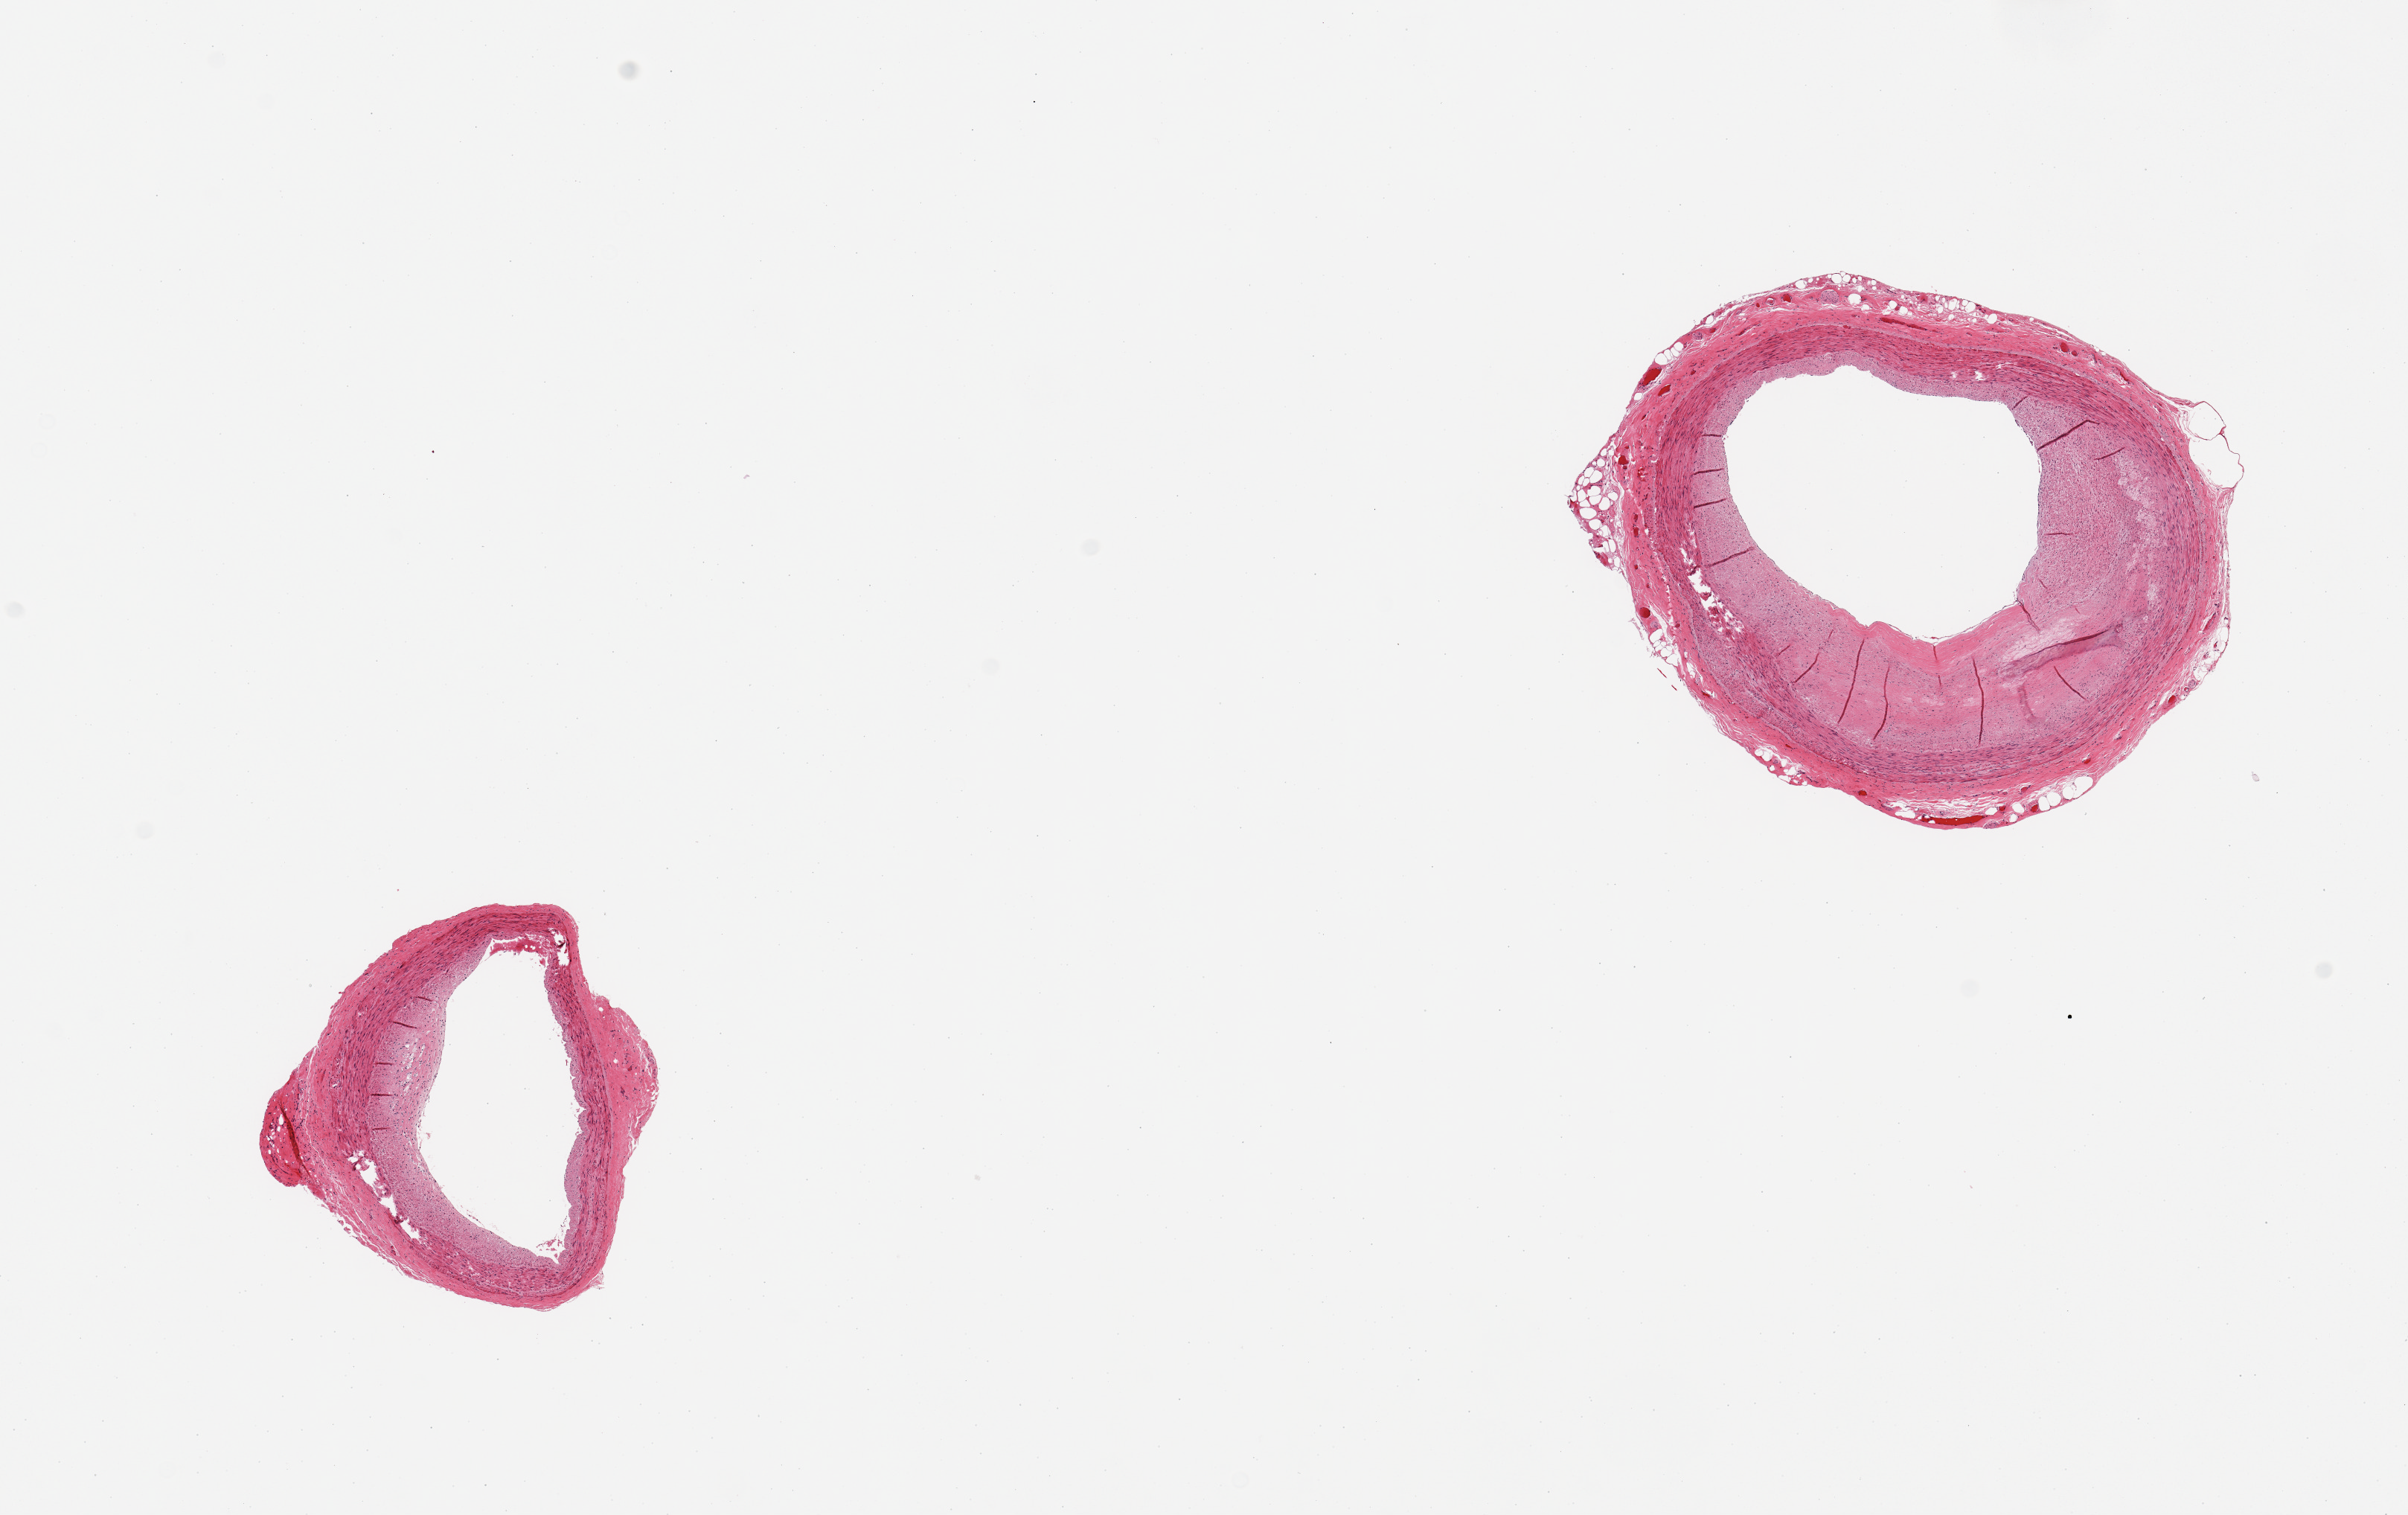
Whole-slide image, haematoxylin and eosin stain — low-resolution overview of the scanned area, about 12.8 x 8.1 mm; PAXgene-fixed paraffin-embedded (PFPE) section; sampled site (target tissue): coronary artery; donor tissue sample. Female donor.
* pathologist's review note for this sample: 2 pieces; mild eccentric plaque; well trimmed